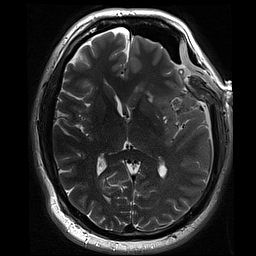
Brain MRI from a brain-tumour surgery series, one axial slice. Position 42 of 70 along the scan axis. 256 × 256 image matrix, field of view 220 × 220 mm. Case-level facts recorded for this patient, not image findings: histopathology: Oligodendroglioma; WHO grade: 3; IDH mutation: yes.
Annotated regions visible in this slice (manually delineated by an expert):
- residual tumour: bounding box <147,92,153,102> (left, top, right, bottom; pixels)